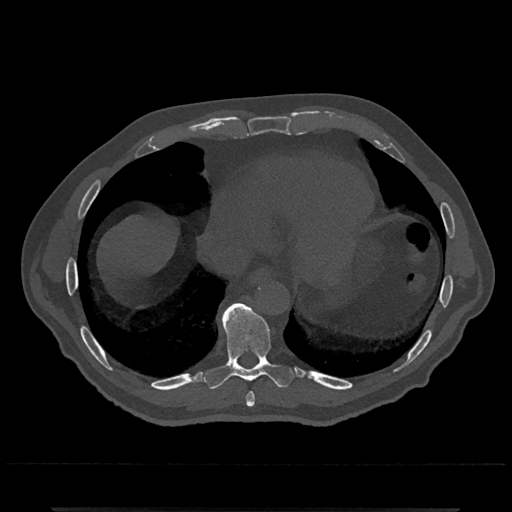
CT including the spine, one axial slice. Position 617 of 797 along the scan axis. 120 kVp. Bone window (W 1800 / L 400 HU). 0.5 mm slice thickness. 512 × 512 image matrix, field of view 393 × 393 mm. Patient: male, 67 years. Case-level facts recorded for this patient, not image findings: primary cancer: prostate.
Structures marked on this image (semi-automatically segmented with operator editing):
- T8 vertebra: bounding box <246,392,255,407> (left, top, right, bottom; pixels)
- T9 vertebra: <204,303,295,390>